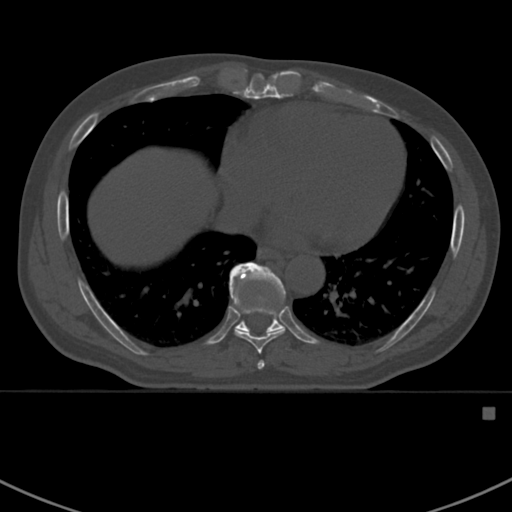
CT including the spine, one axial slice; position 394 of 412 along the scan axis; reconstruction kernel Br40s; bone window (W 1800 / L 400 HU); 512 × 512 image matrix, field of view 358 × 358 mm. Patient: male, 59 years. From the clinical record (not read from this slice): primary cancer: prostate.
Annotated regions visible in this slice (semi-automatically segmented with operator editing):
- T7 vertebra: bounding box [x1, y1, x2, y2] px = [257, 360, 265, 369]
- T8 vertebra: [235, 329, 285, 354]
- T9 vertebra: [229, 262, 287, 333]